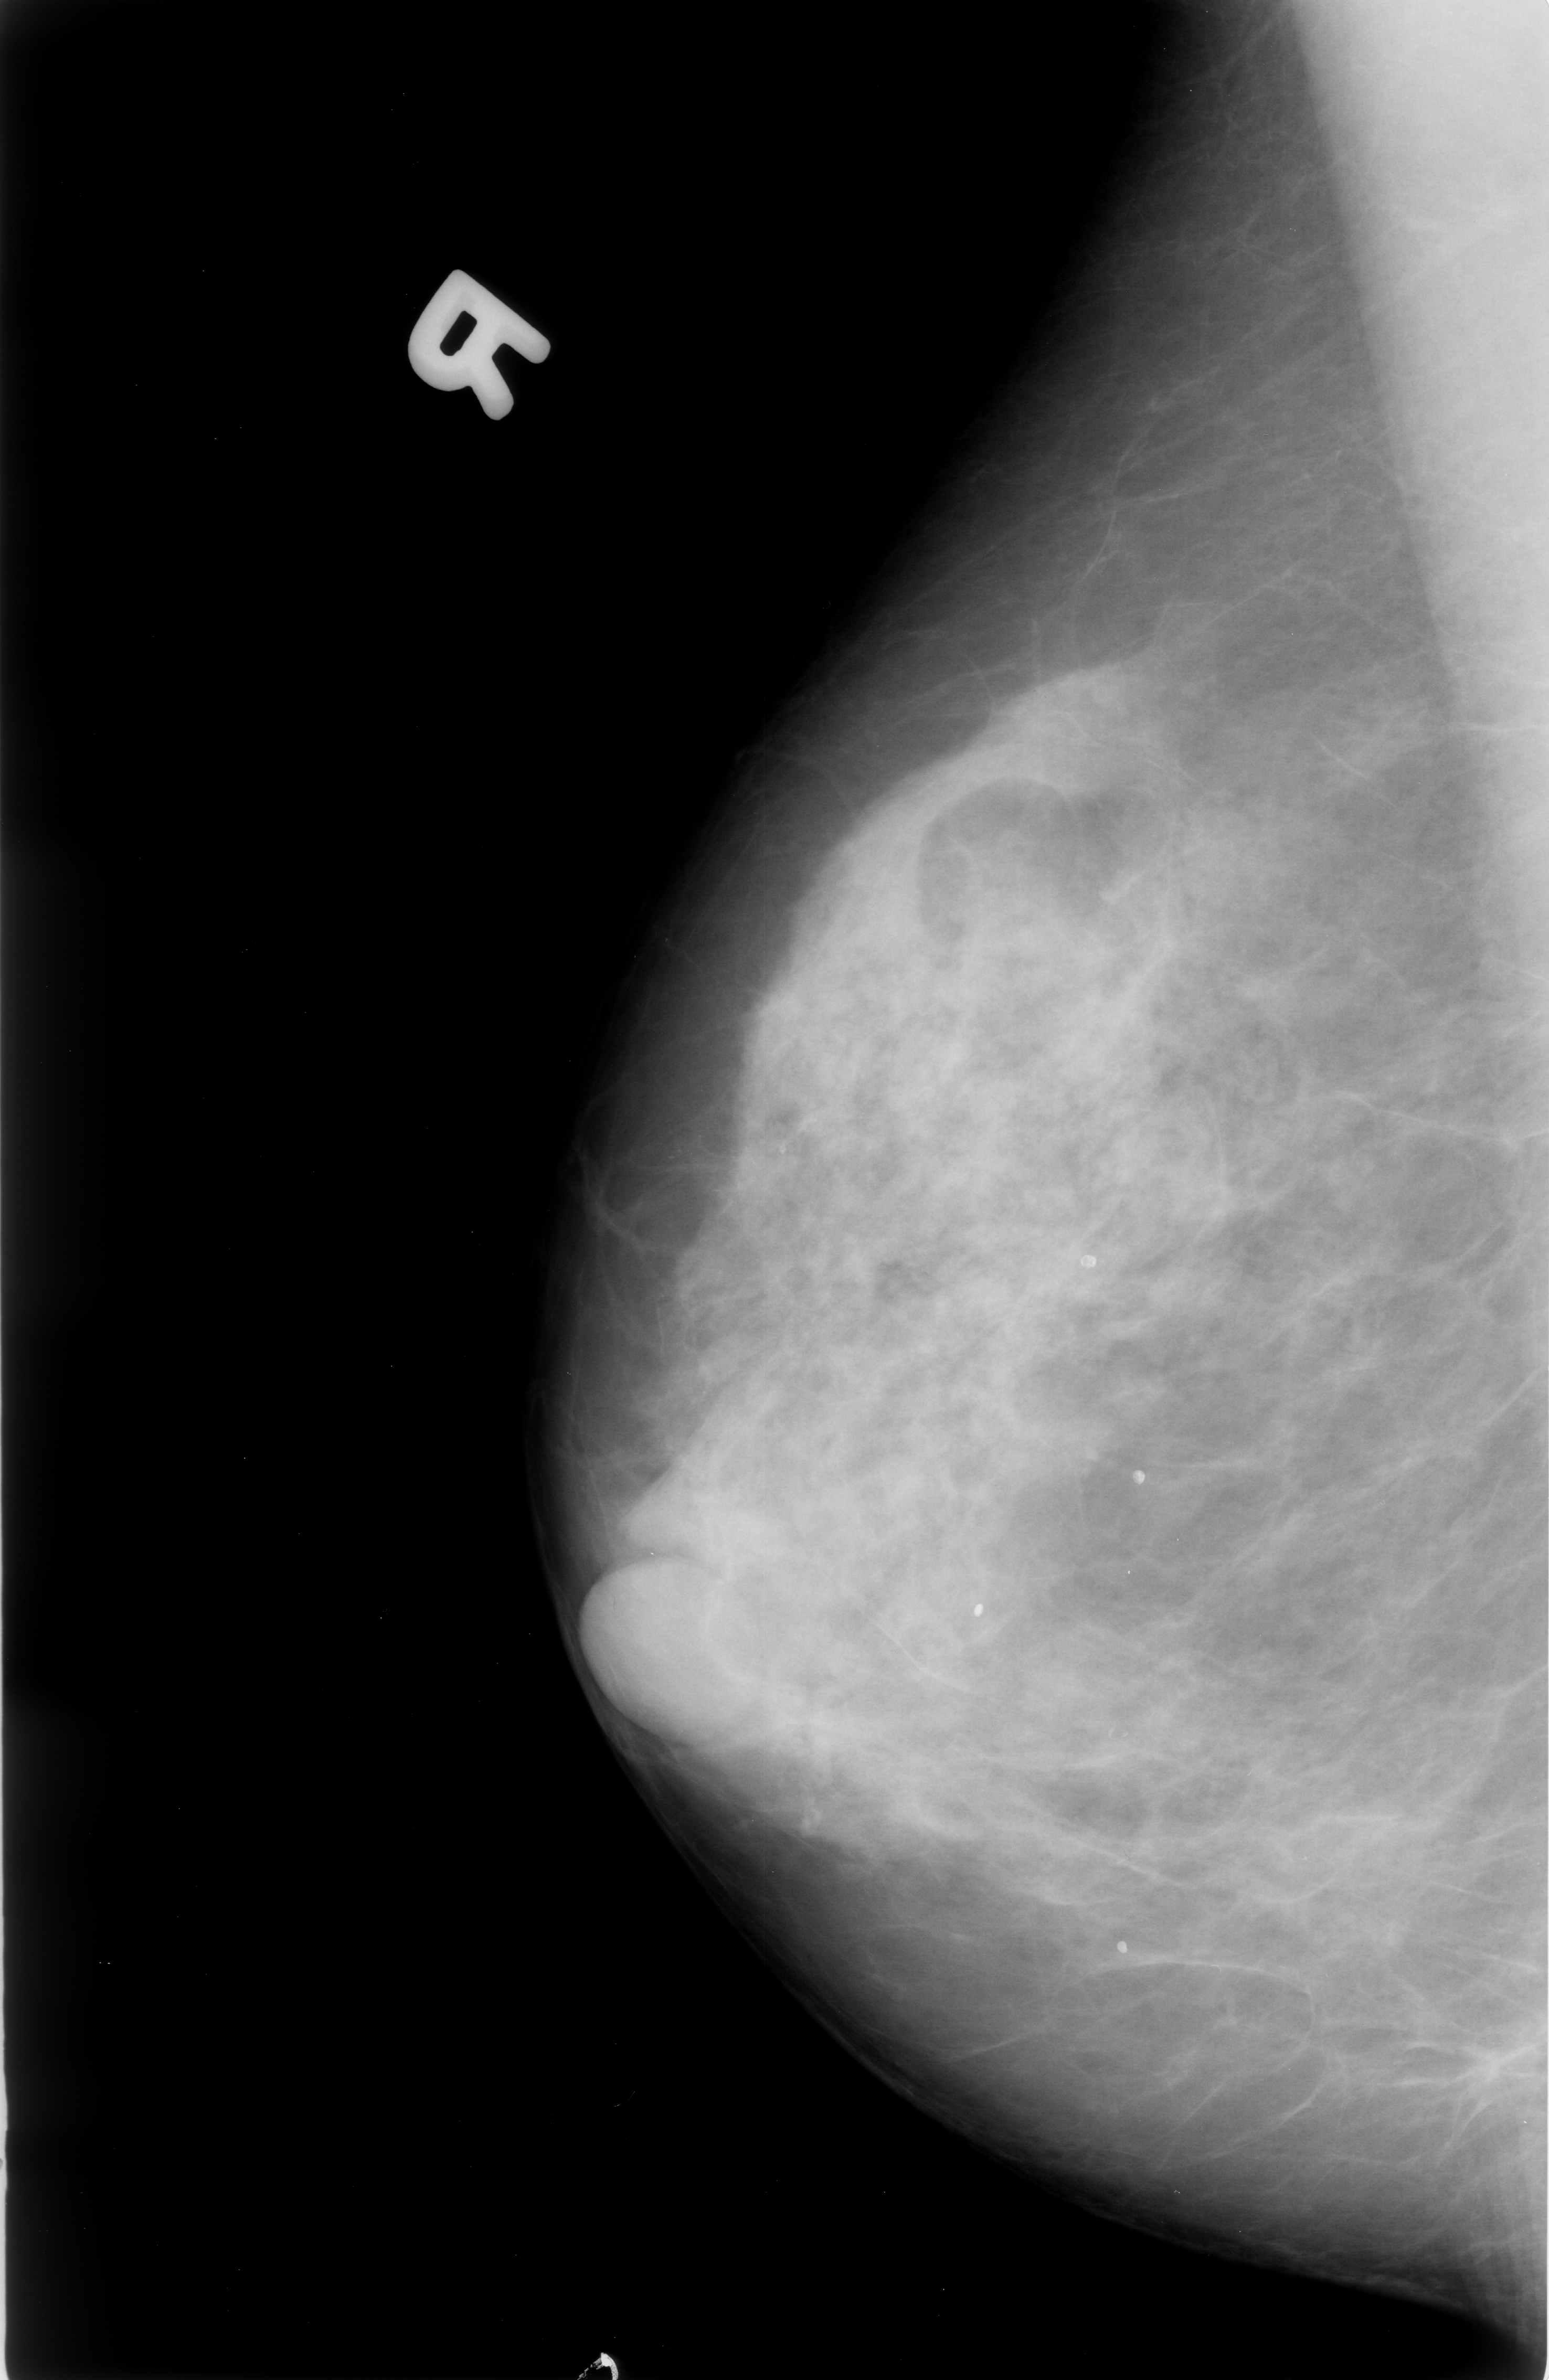
Scanned film-screen mammogram; right breast; MLO view; 1549 × 2380 image matrix.
Expert-marked regions of interest on this image (one box per marked abnormality):
- calcifications, morphology punctate / pleomorphic, distribution clustered; BI-RADS assessment category 3; subtlety rating 2 on a 1 (subtle) to 5 (obvious) scale; pathology (as recorded): malignant: bounding box <881,1015,979,1139> (left, top, right, bottom; pixels)